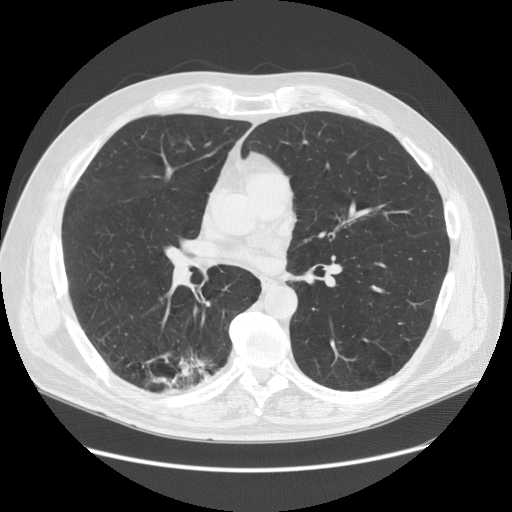
Low-dose screening chest CT, one axial slice. Slice 75 of 149 in the series (ordered by position). Reconstruction kernel STANDARD. Lung window (W 1500 / L -600 HU). 512 × 512 image matrix, field of view 400 × 400 mm.
Structures marked on this image (manually delineated by an expert):
- lesion 1 (tumor, lower lobe of right lung): bounding box (x1, y1, x2, y2) in pixels: (153, 357, 211, 391)